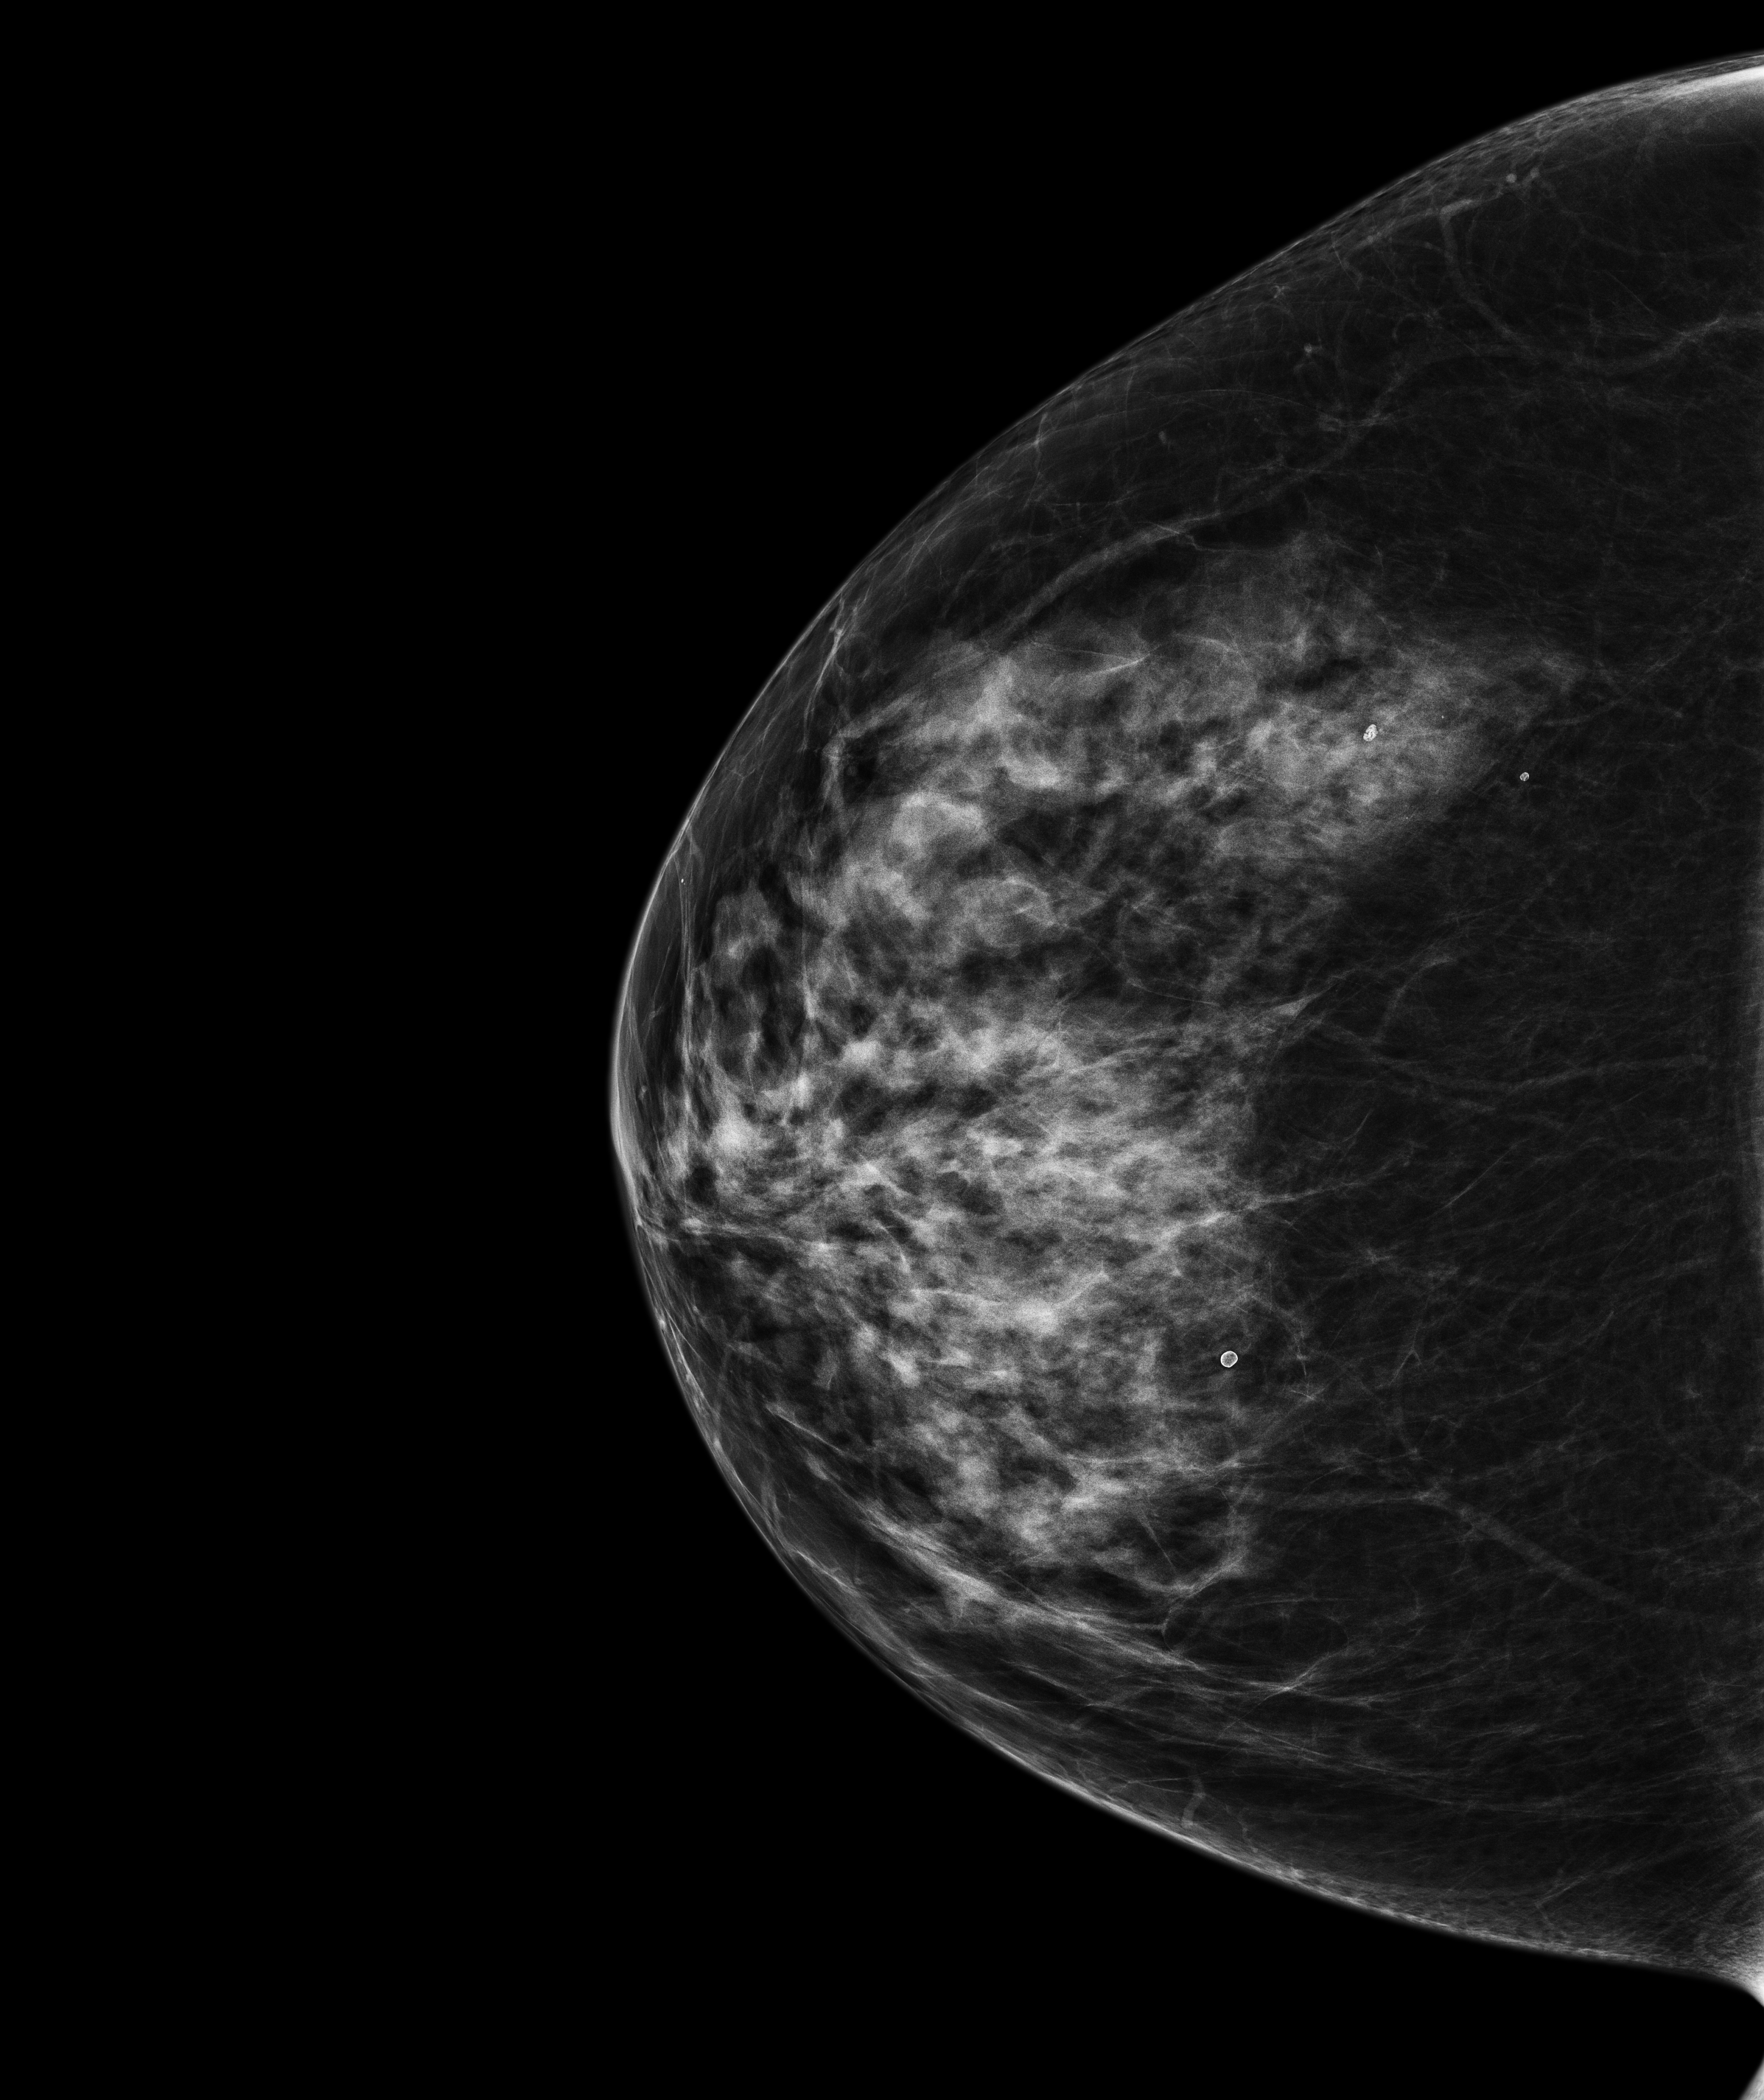
Screening examination, compressed breast thickness 59.6 mm, system: Senographe Pristina. Patient: female, 66 years.
Image type: full-field digital mammogram. Breast: right. Projection: craniocaudal (CC) view.